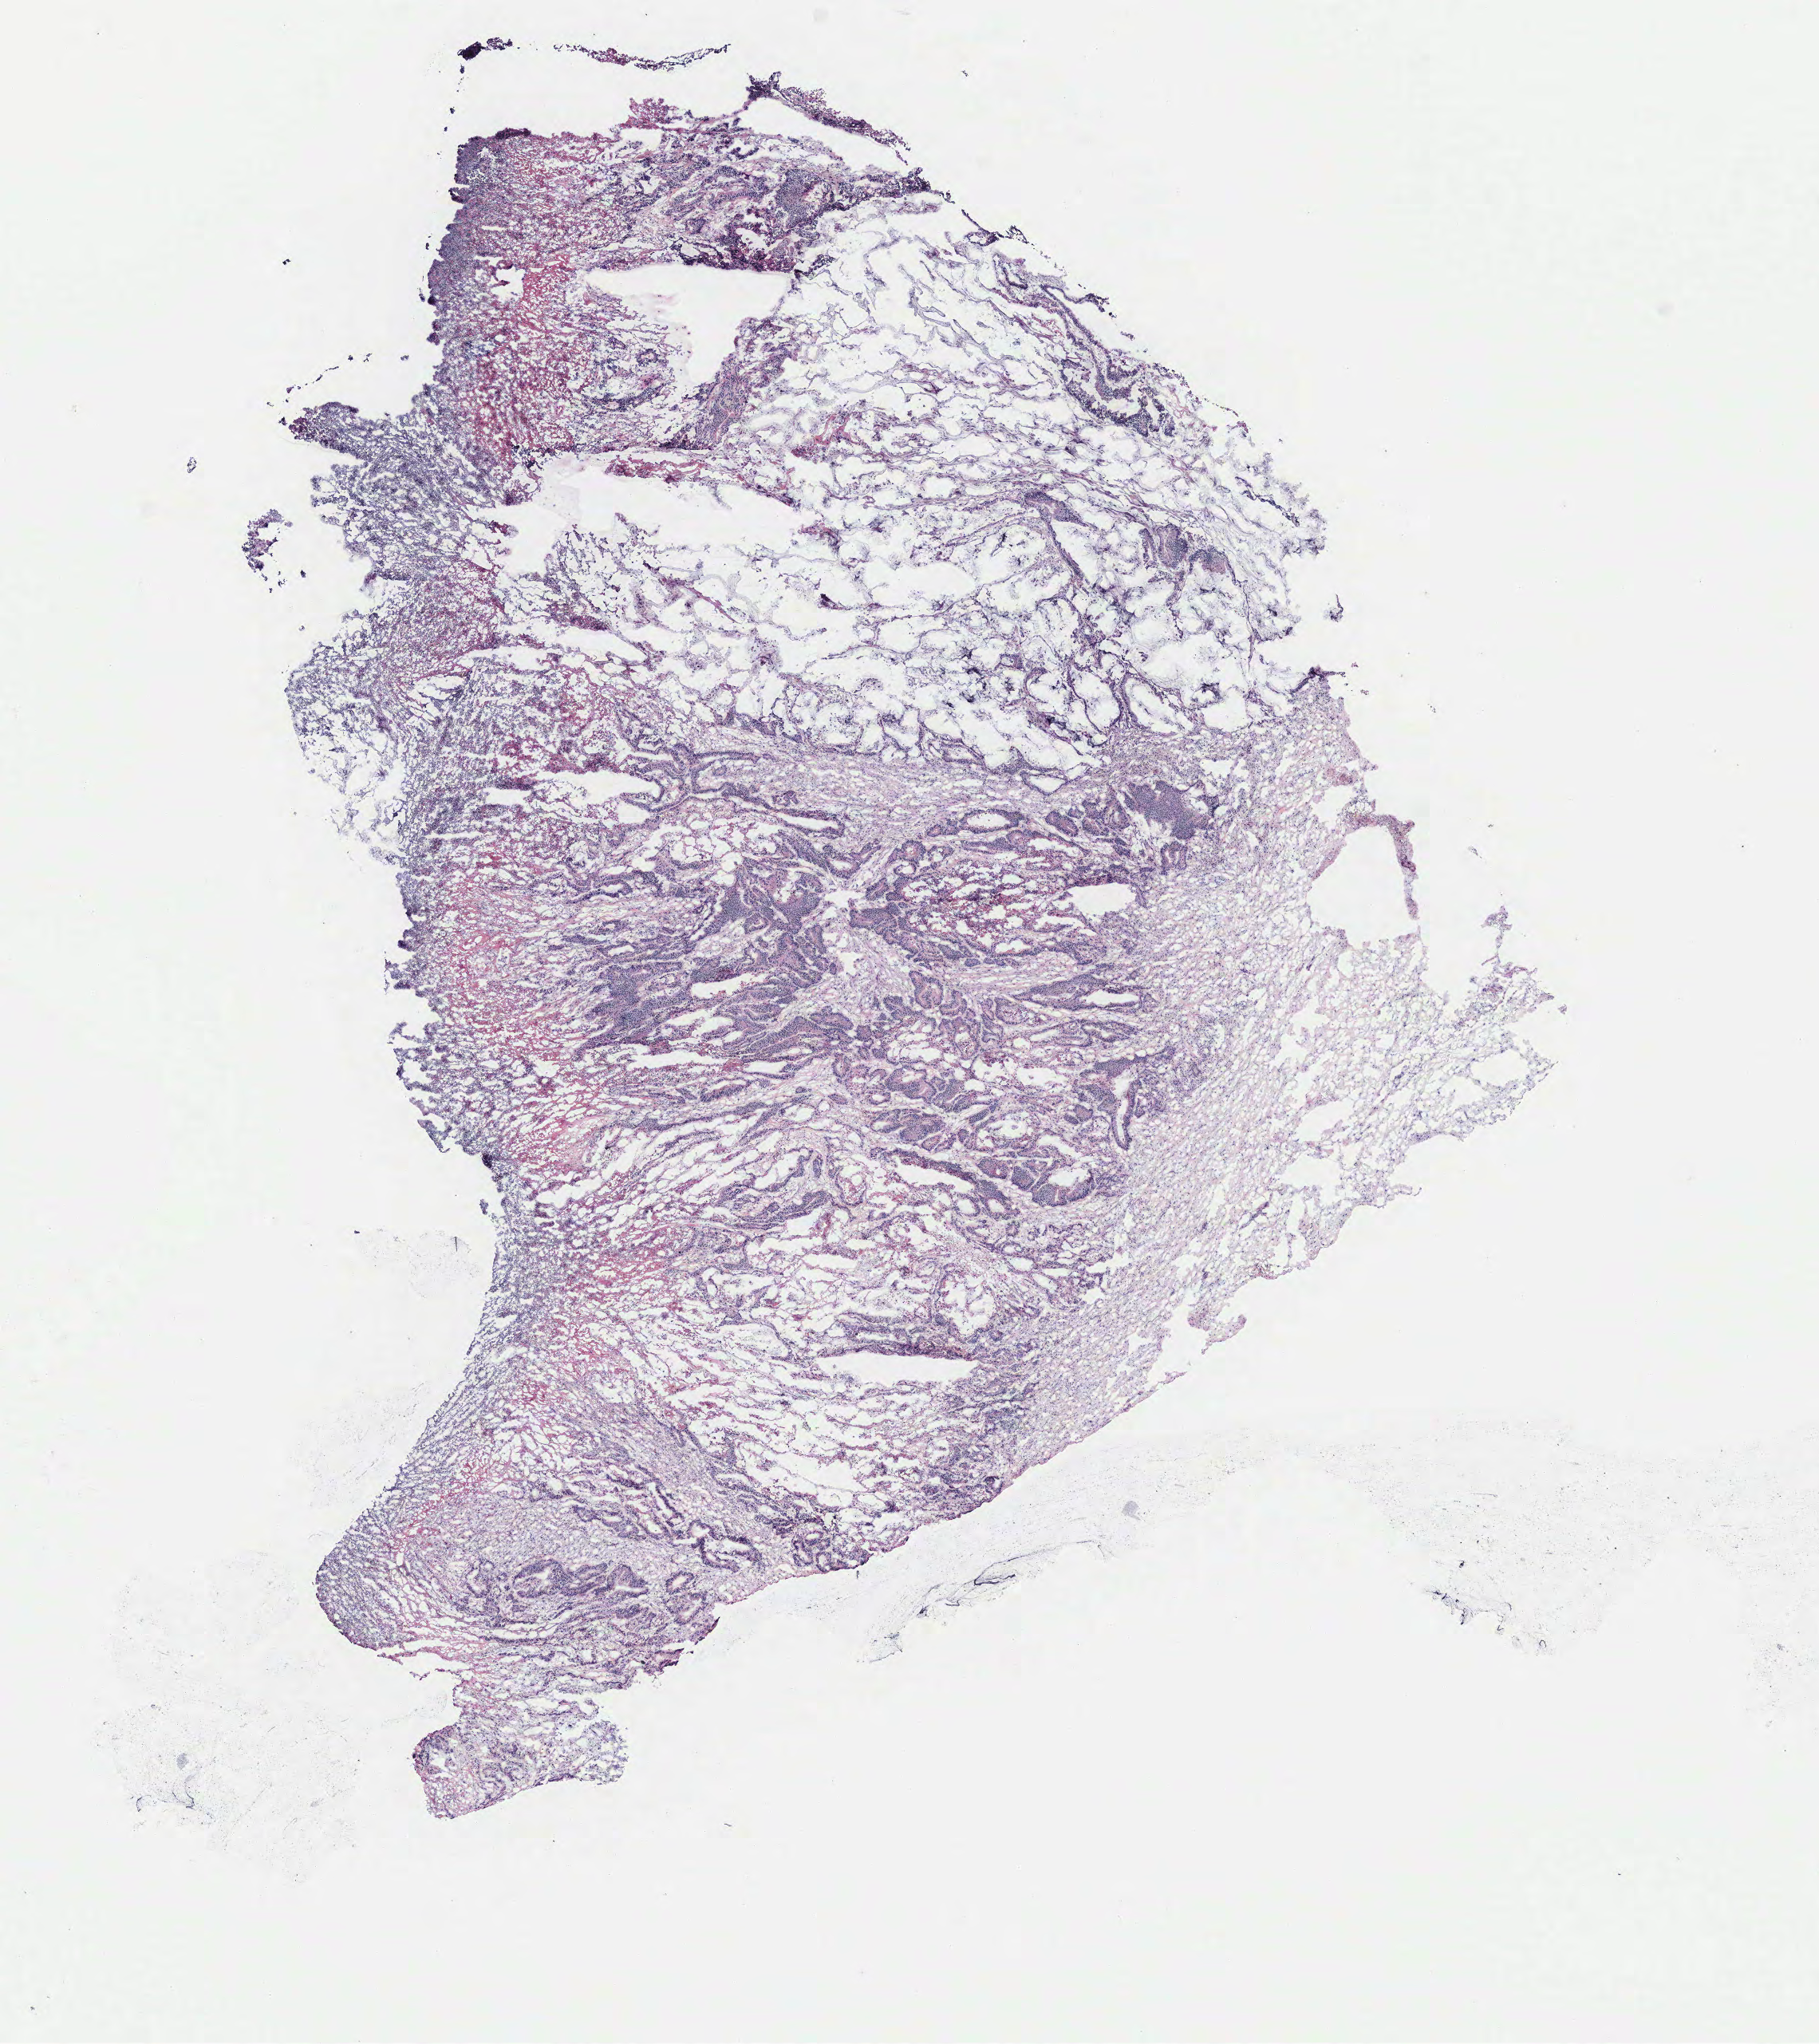
Digitized Hematoxylin and eosin (H&E) stained tissue section (whole slide) — whole scanned area (about 9.1 x 10.3 mm, from a 40x scan) shown as a low-resolution overview. Colon, normal (non-tumour) tissue. Patient sex: male.
This section: normal (non-tumour) tissue from the same patient. Patient diagnosis: Adenocarcinoma, NOS.